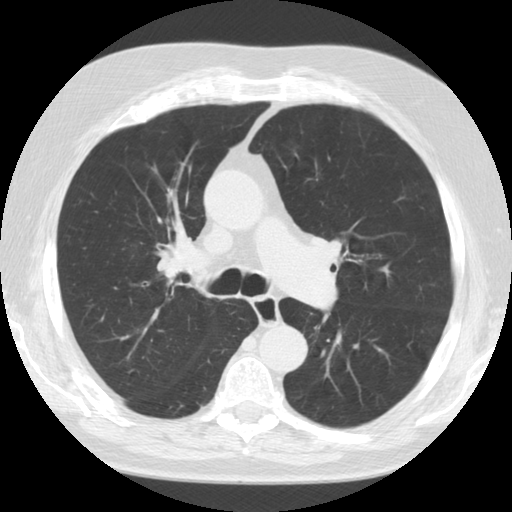
Axial slice from a low-dose chest CT screening exam, baseline annual screen, lung window (W 1500 / L -600 HU), 512 × 512 image matrix, field of view 340 × 340 mm. Male, age 72 years at enrolment.
Lesion marked by an expert reader, bounding box (x1, y1, x2, y2) in pixels: (138, 224, 217, 297). No non-calcified nodule or mass ≥4 mm was recorded by the screening reader at this exam.